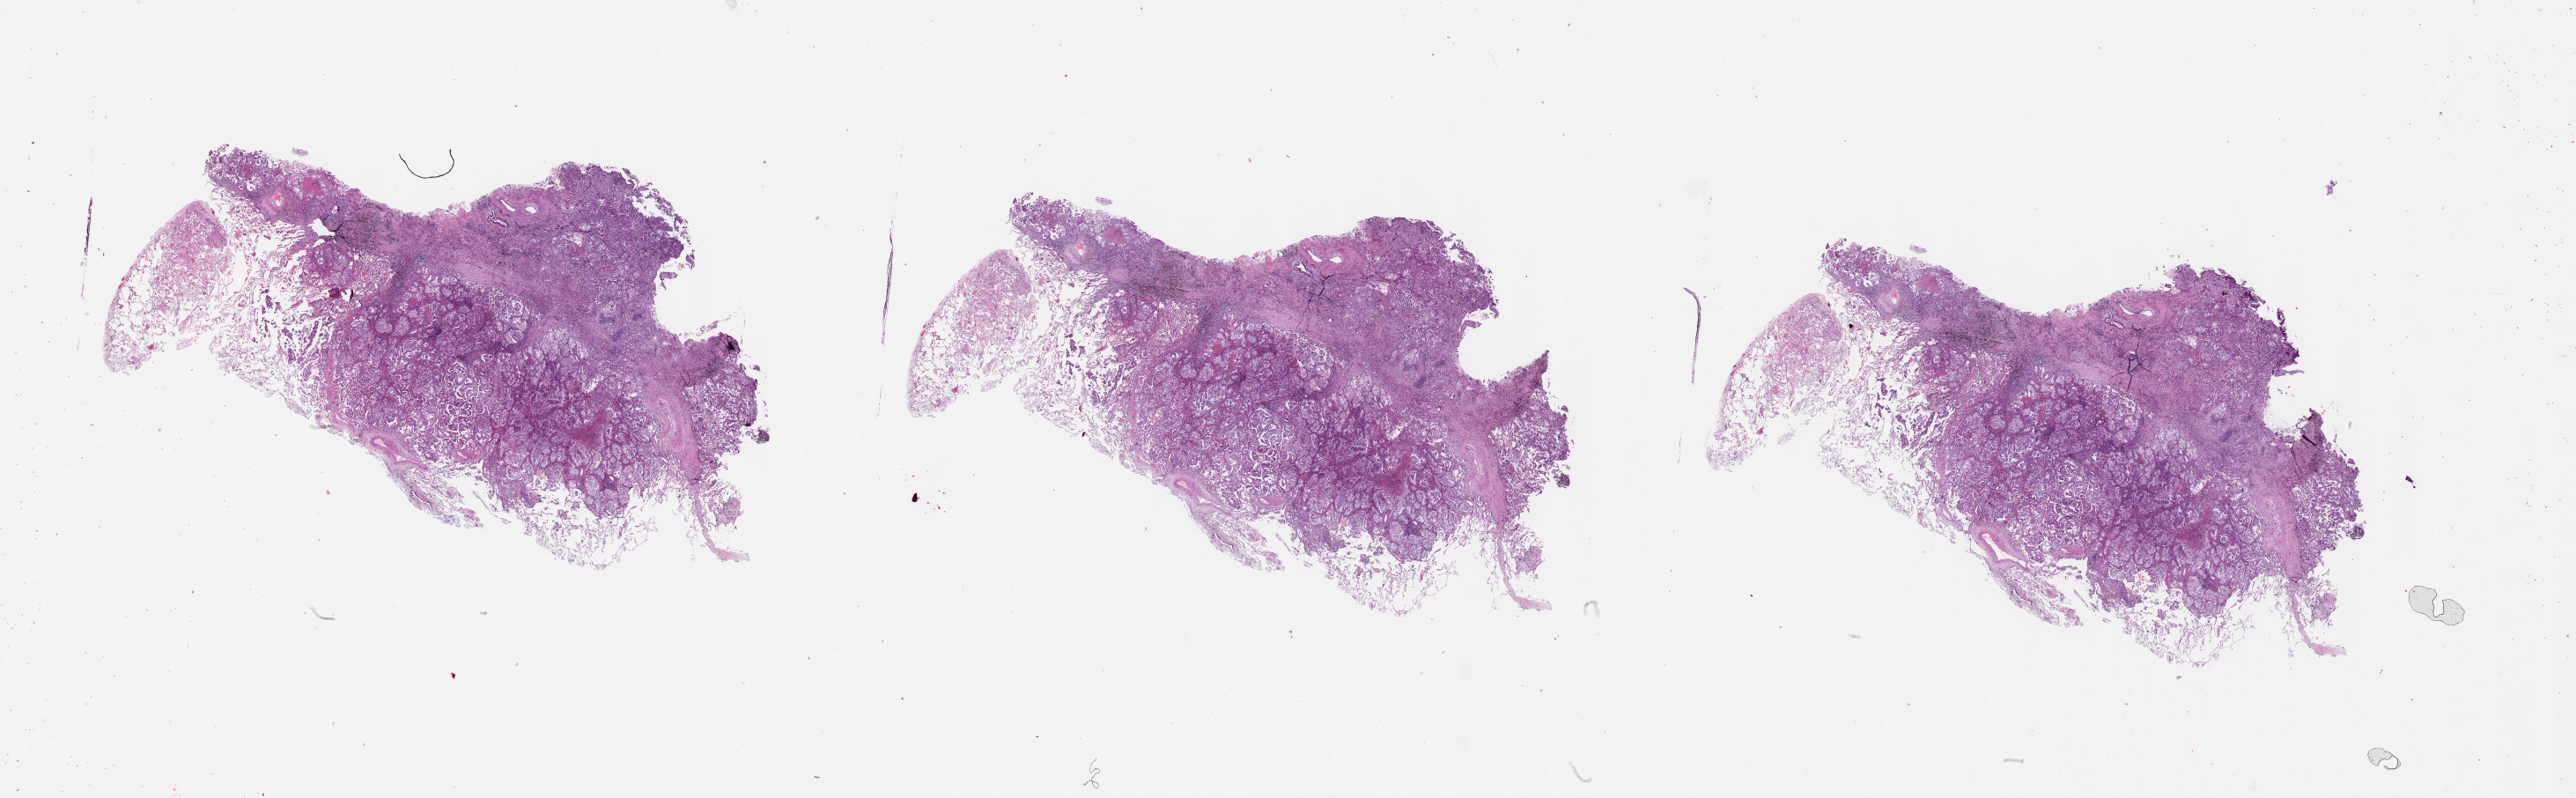
Digitized H&E tissue section (whole slide) — low-resolution overview of the scanned area, about 47.1 x 14.6 mm (slide scanned at 20x). Lung, tissue type not recorded.
Patient diagnosis (cohort enrolment): lung adenocarcinoma (lung).